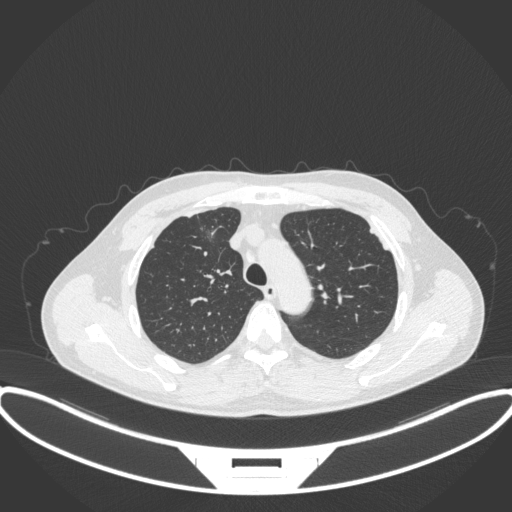
Chest CT, one axial slice. Slice 273 of 395 in the series (ordered by position). Lung window (W 1500 / L -600 HU). 1 mm slice thickness. 512 × 512 image matrix. Patient: male, 60 years. From the clinical record (not read from this slice): clinical TNM (as recorded): T1c N0 M0.
Outlined on this slice (bounding box drawn by a radiologist):
- lung tumour (recorded histology: adenocarcinoma): bounding box [x1, y1, x2, y2] px = [190, 212, 226, 247]